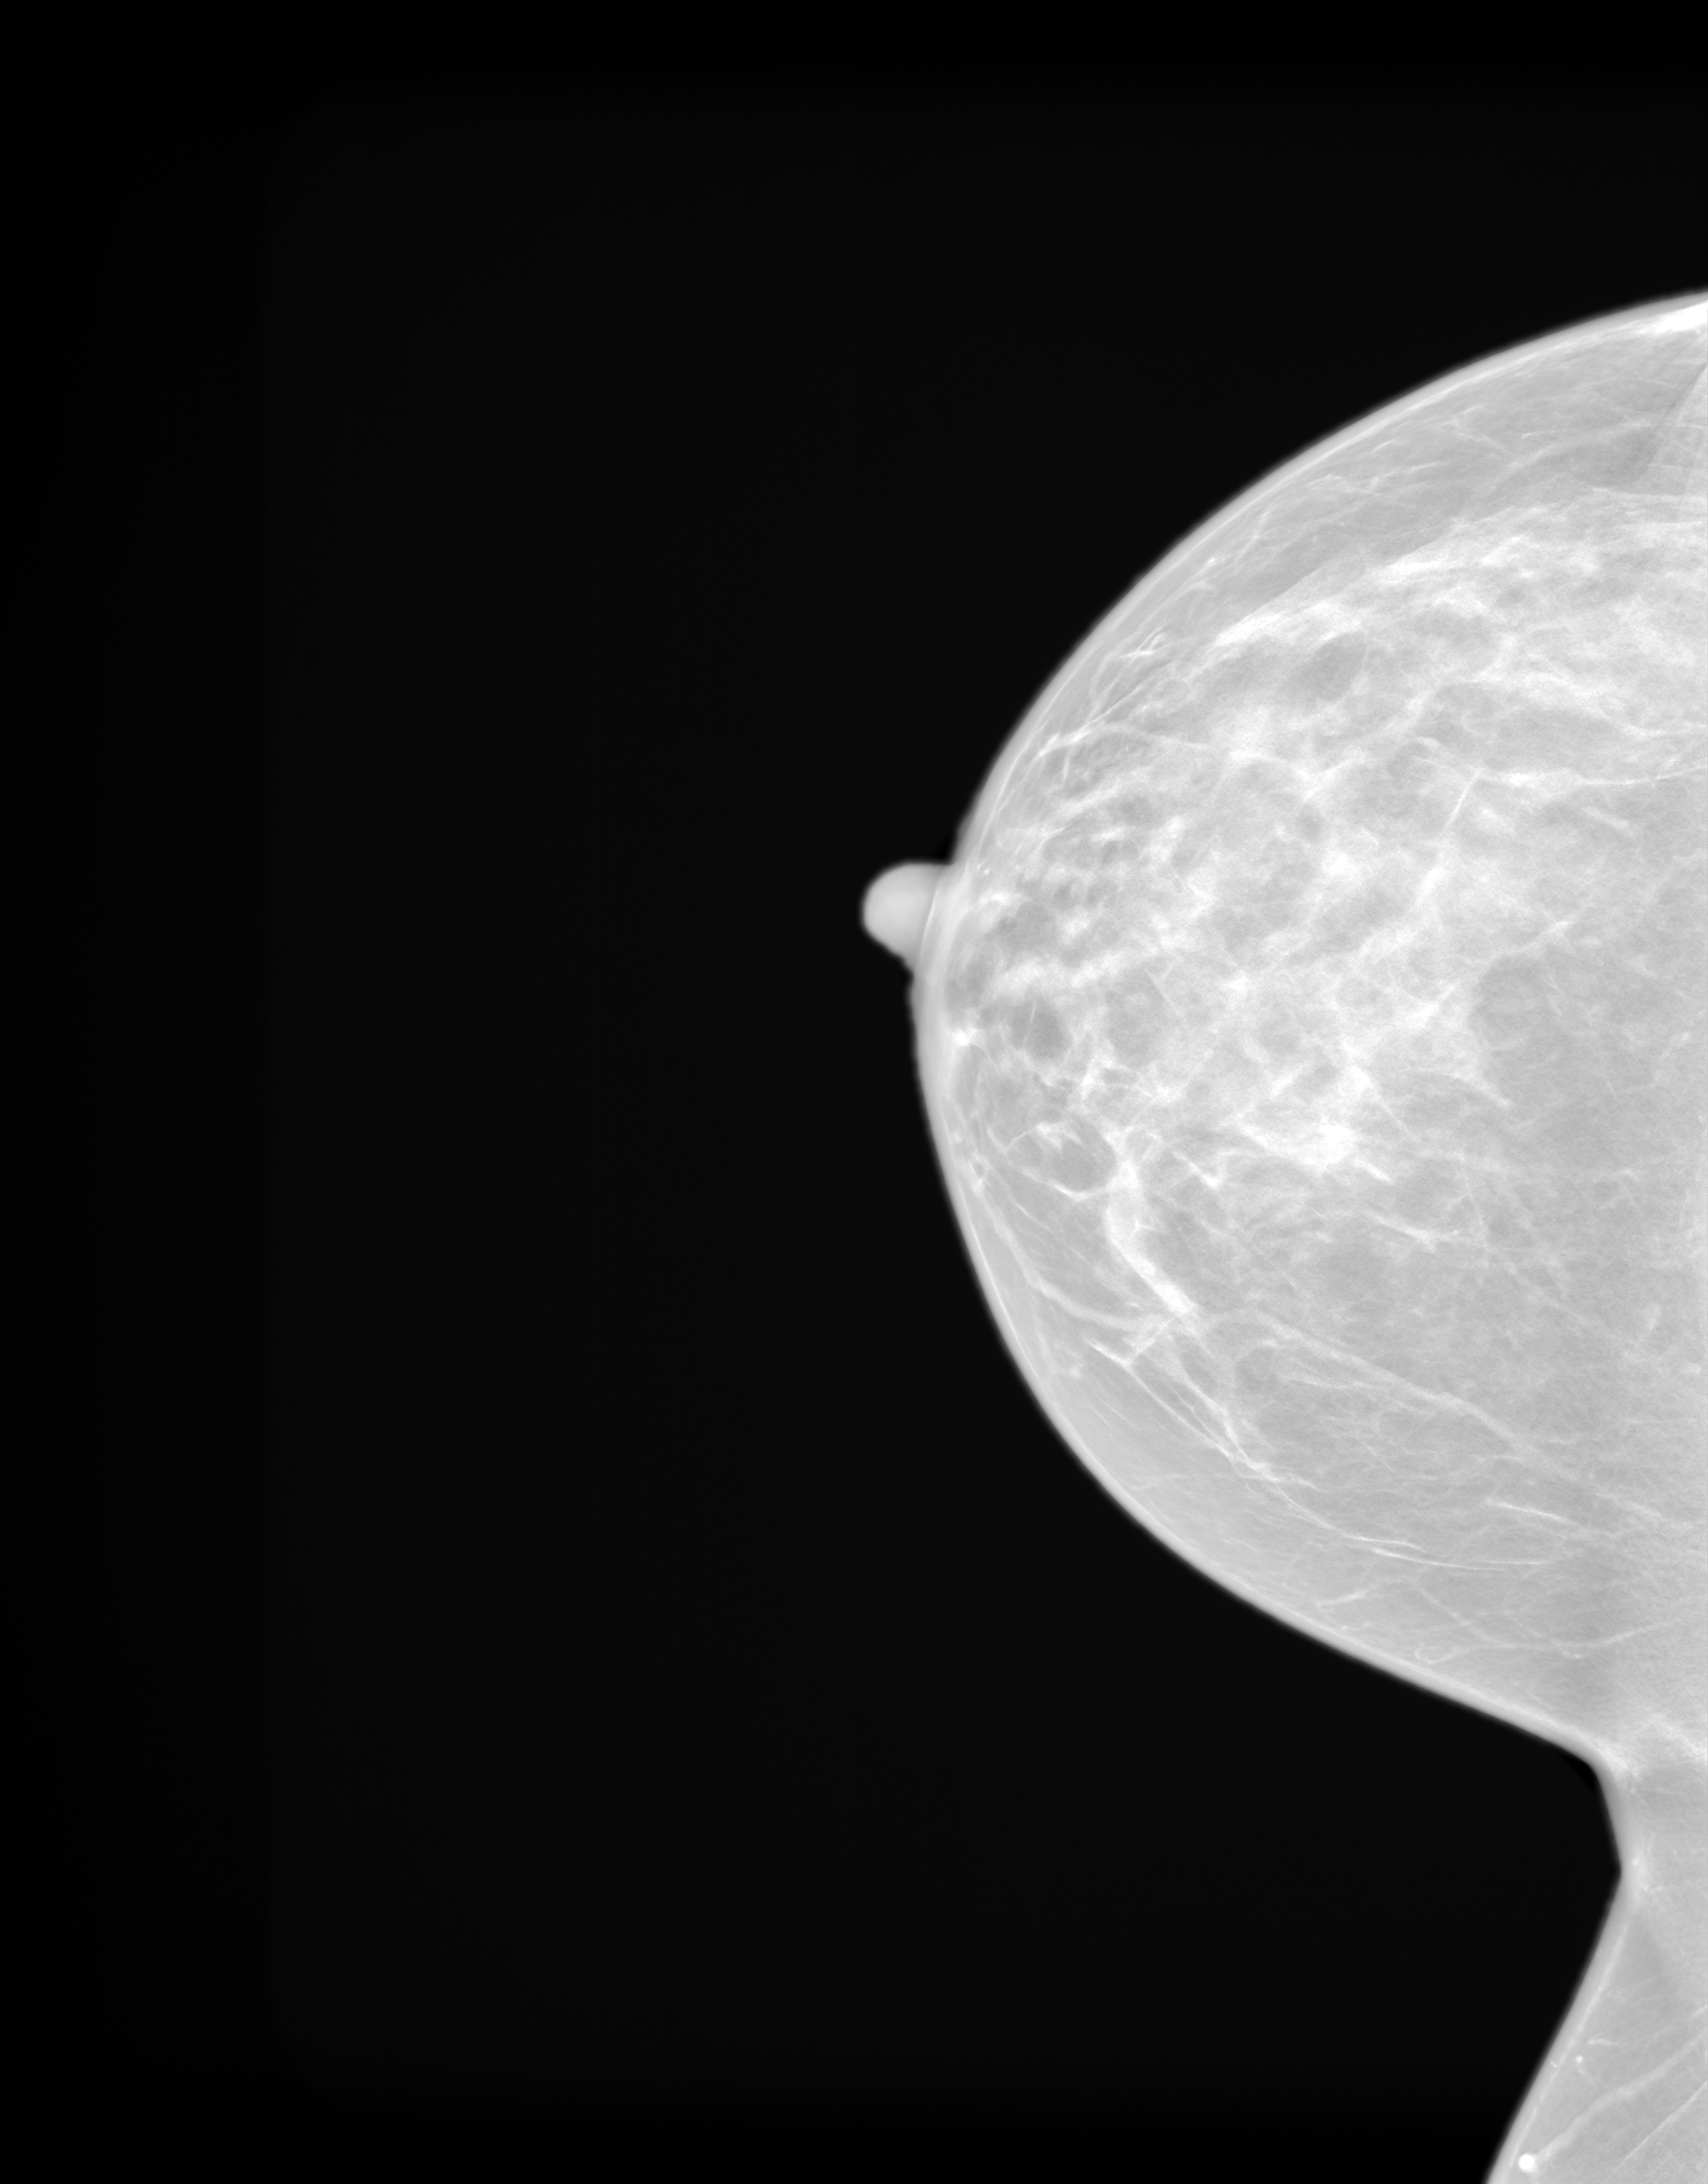
Annual screening mammography examination. Patient: female, 50 years.
Image type: synthesized 2-D view from tomosynthesis. Breast: right. Projection: craniocaudal (CC) view.